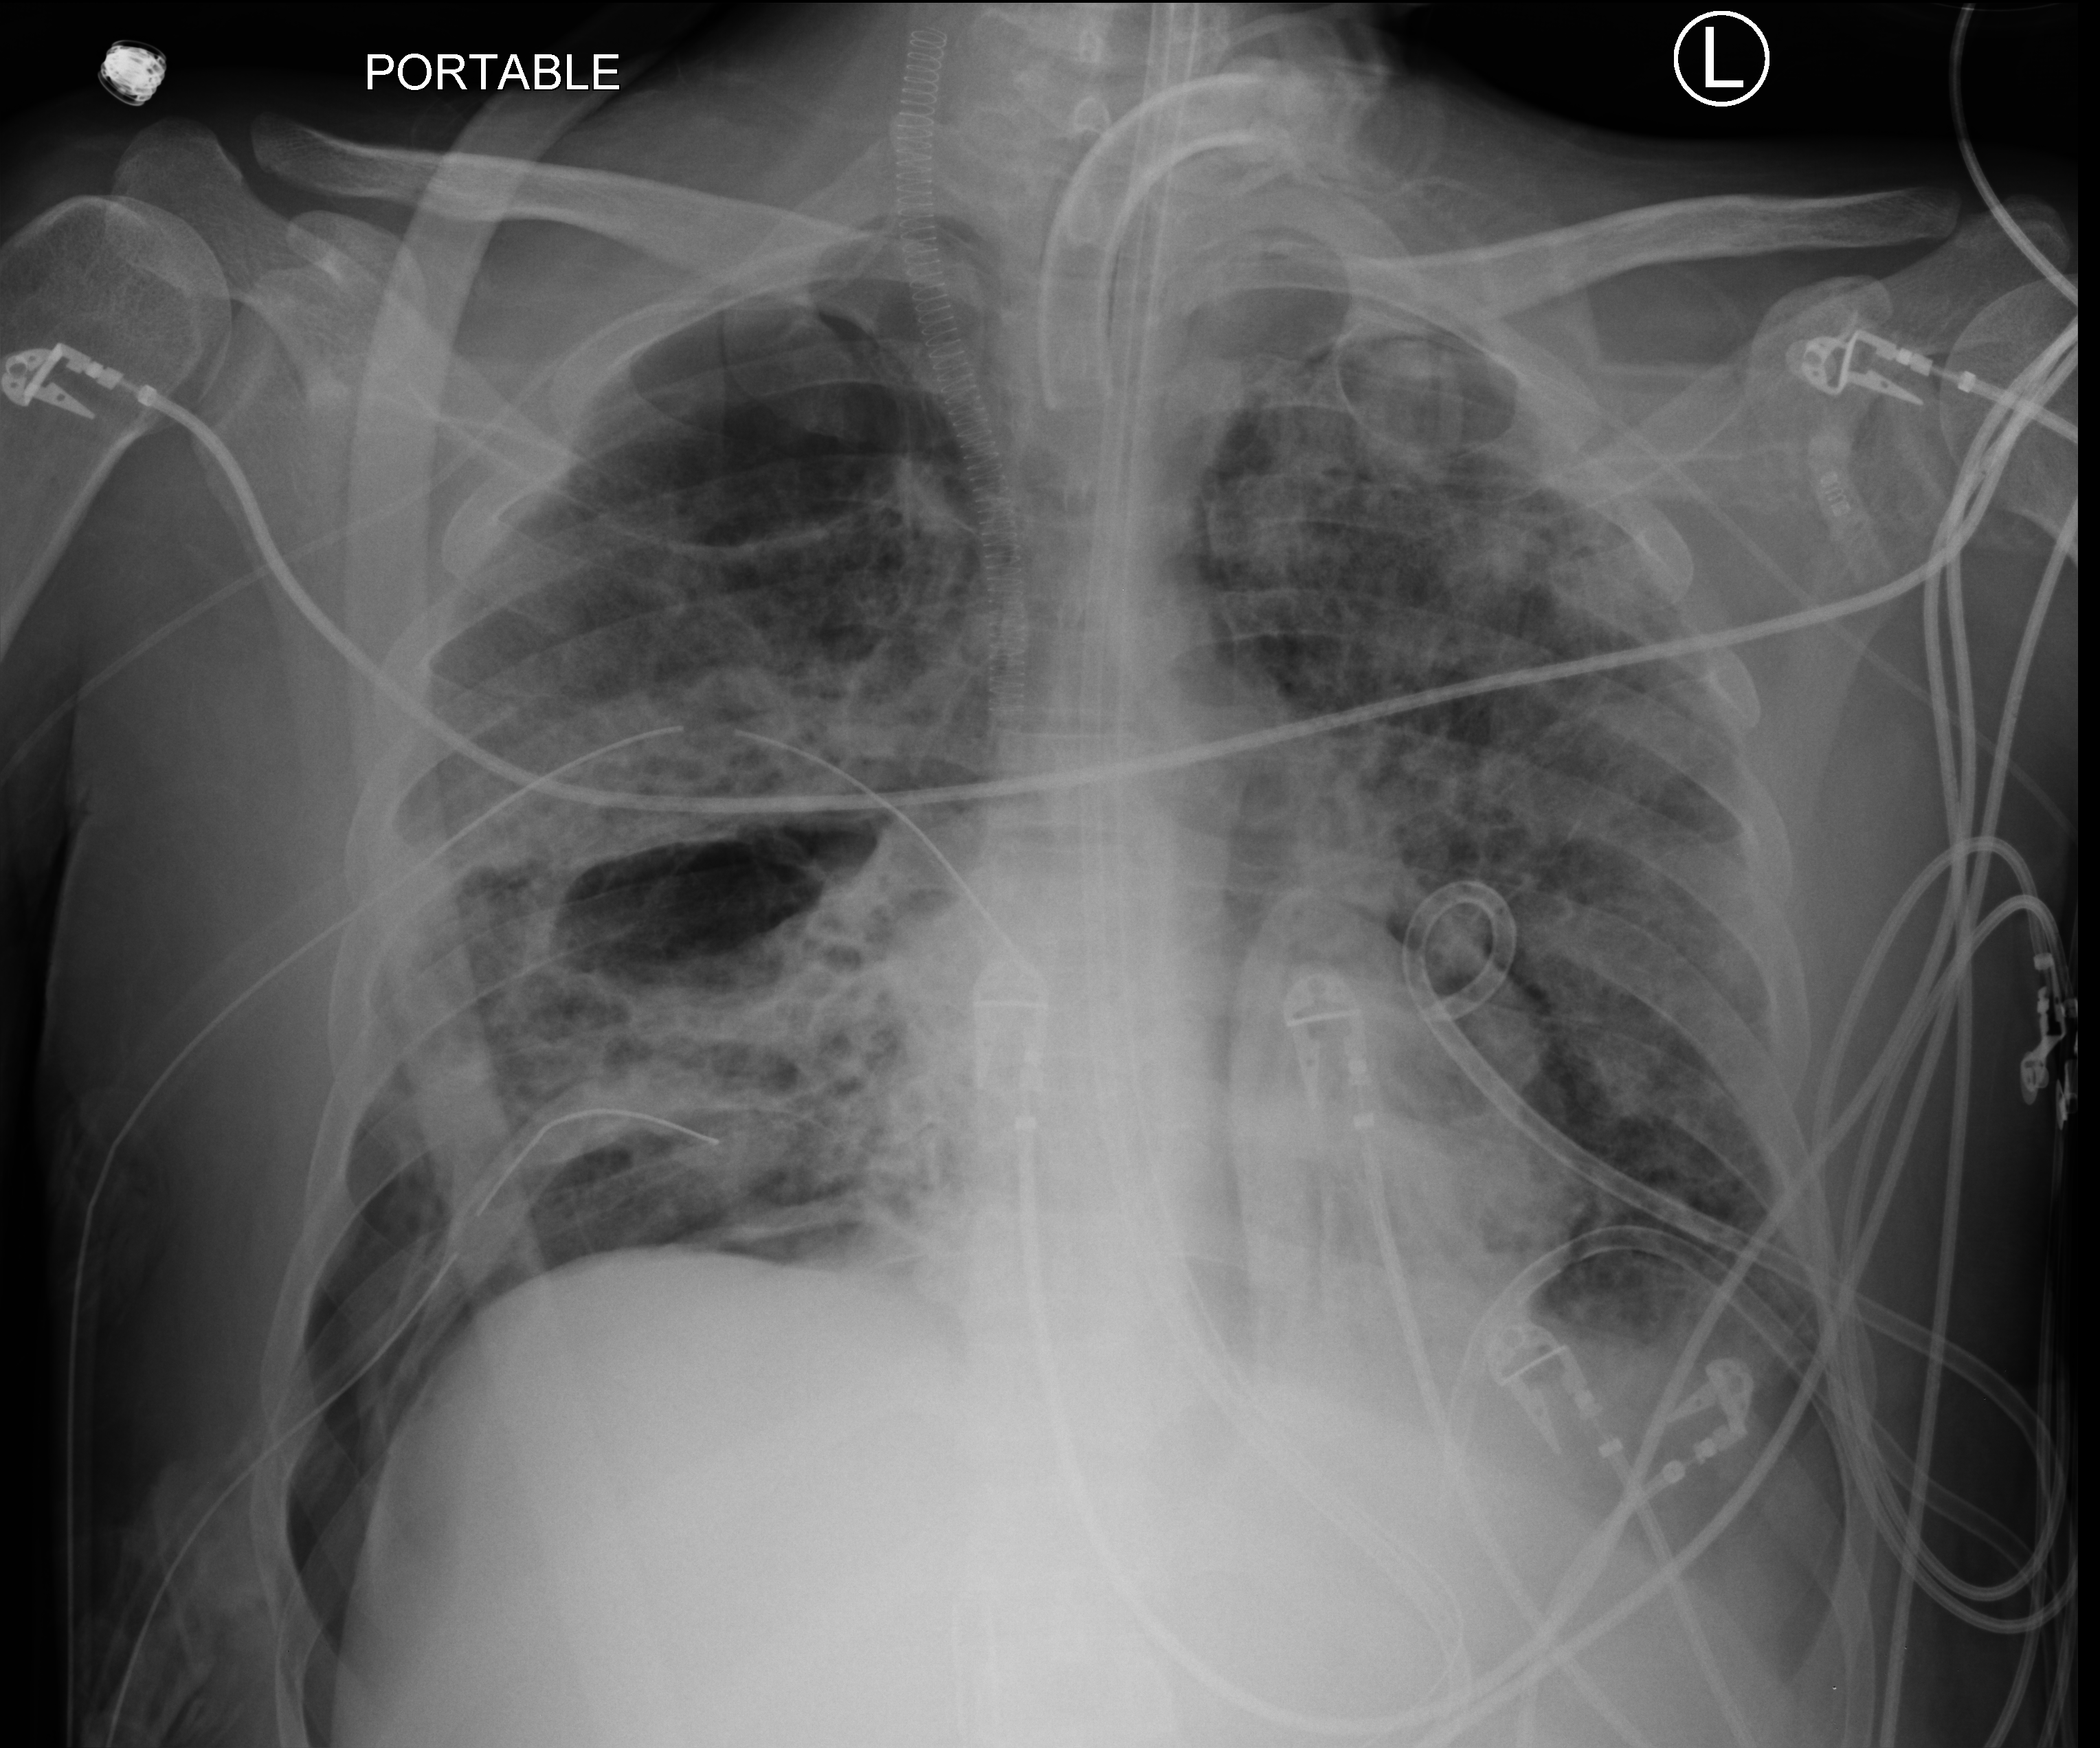
Bedside chest radiograph (computed radiography). Adult patient hospitalised with COVID-19, age 18–59 years.
Hospital-stay facts (about this admission, not read from this image; timing relative to this image not recorded): length of hospital stay: 60 days; diabetes (admission record): no.